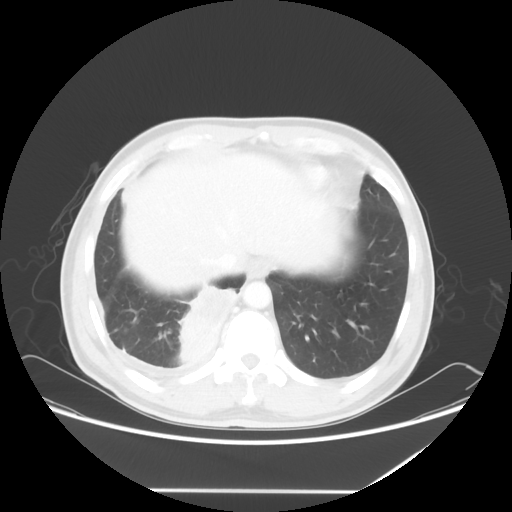
Chest CT, one axial slice; position 14 of 60 along the scan axis; reconstruction kernel STANDARD; lung window (W 1500 / L -600 HU); 5 mm slice thickness; 512 × 512 image matrix, field of view 419 × 419 mm. Male patient, age 48 years. From the clinical record (not read from this slice): clinical TNM (as recorded): T3 N3 M1a.
Outlined on this slice (rectangle marked by the reading radiologist):
- lung tumour (recorded histology: squamous cell carcinoma): bounding box <175,279,240,364> (left, top, right, bottom; pixels)